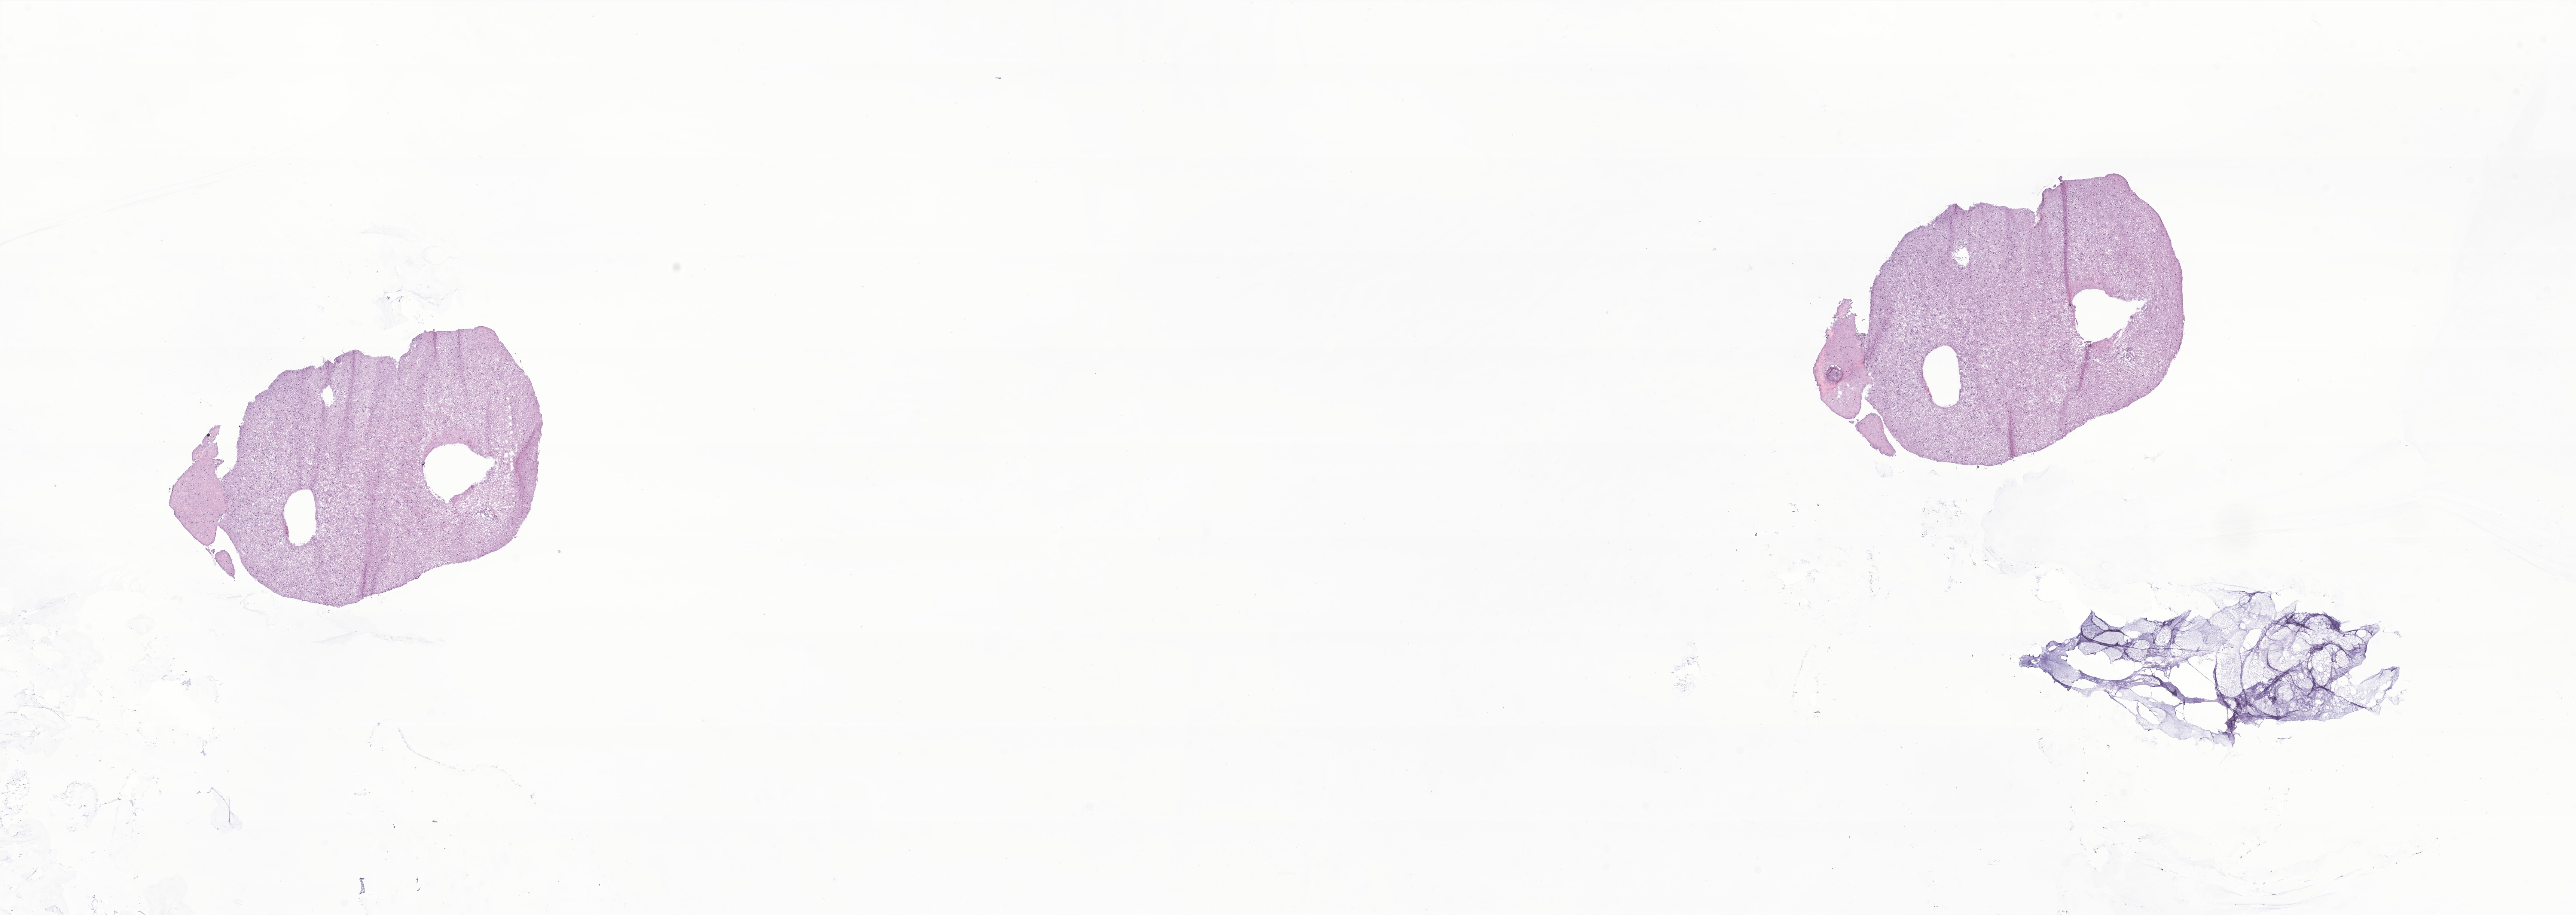
Whole-slide image, hematoxylin and eosin (H&E) stain of tumor tissue from the brain, a low-resolution overview of the entire scanned area, about 29.0 x 10.3 mm. Frozen section. Male patient, age 84 months.
Diagnosis (ICD-O-3 morphology term): Glioma, malignant.